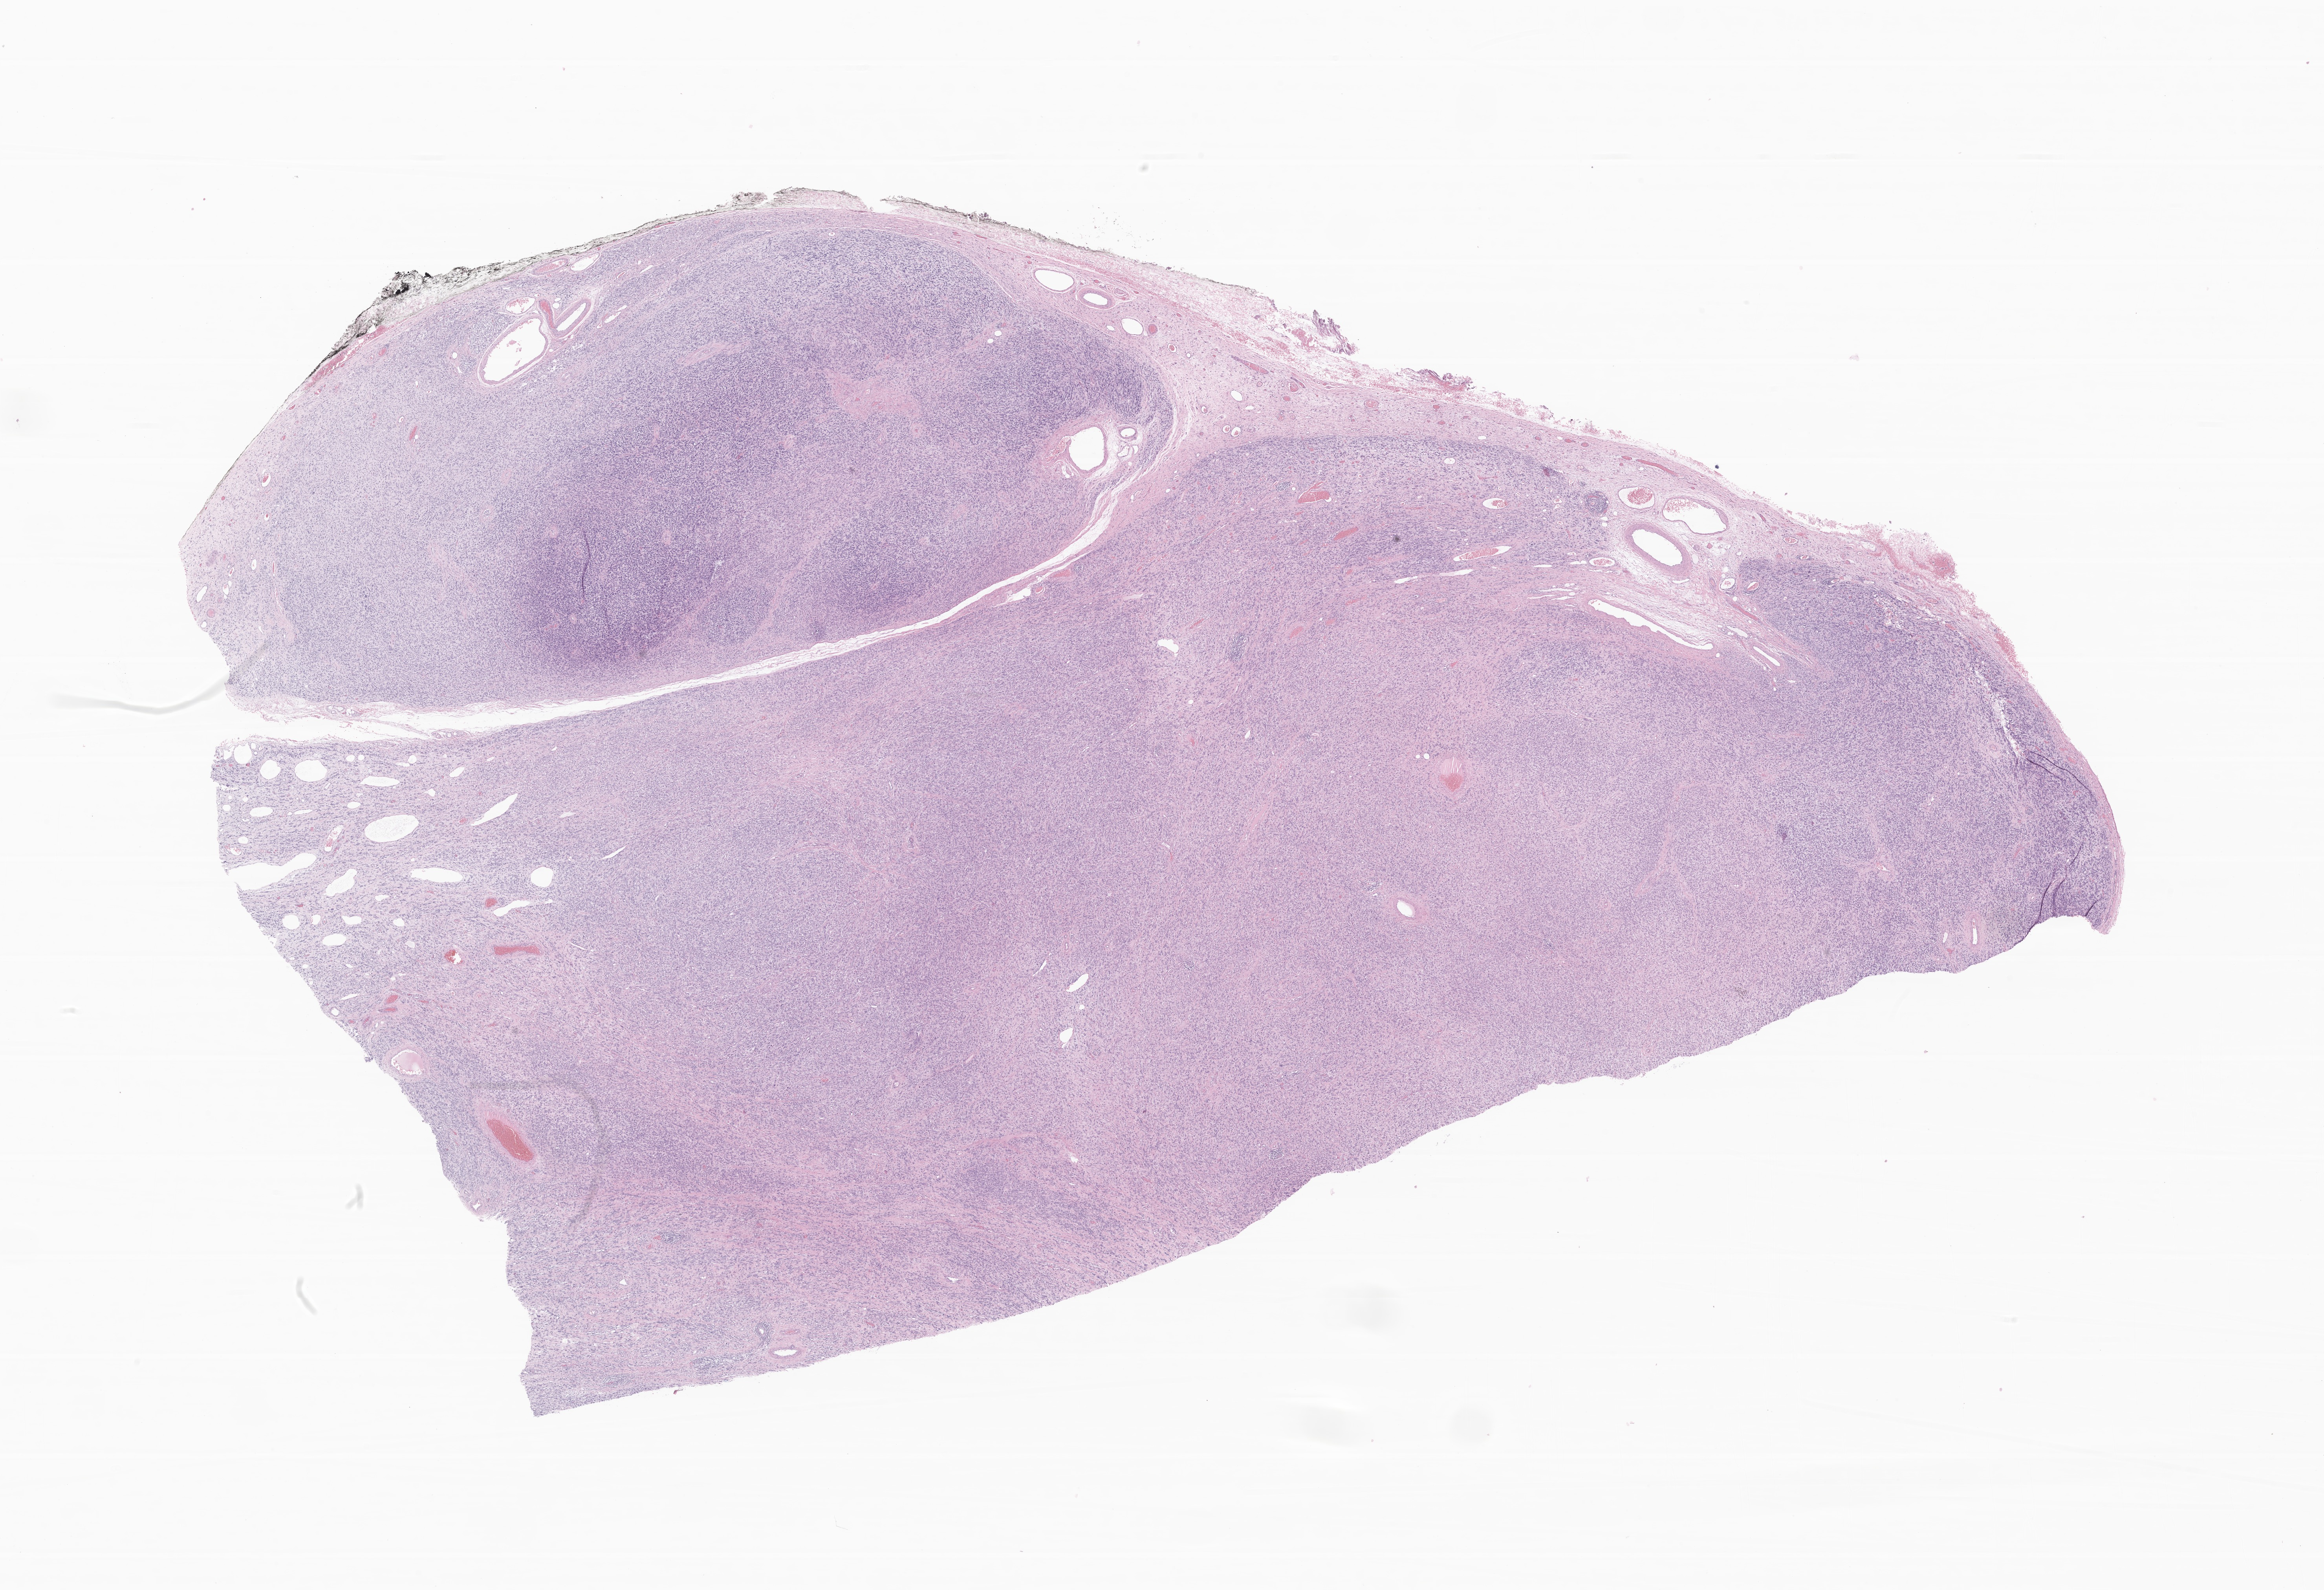
Digitized haematoxylin and eosin-stained section of tumor tissue from the testis, shown as a low-resolution overview of the whole scanned area (about 24.9 x 17.1 mm); formalin-fixed paraffin-embedded section. Patient male; age 198 months (16 years 6 months).
Recorded diagnosis: Embryonal rhabdomyosarcoma, NOS.